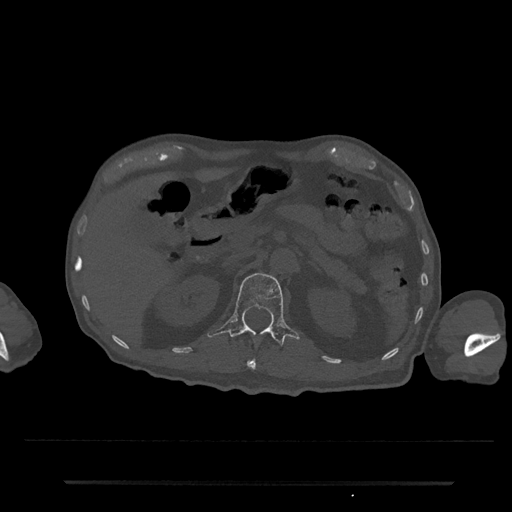
CT including the spine, one axial slice. Position 142 of 797 along the scan axis. Reconstruction kernel Br40s/3. Bone window (W 1800 / L 400 HU). 0.5 mm slice thickness. 512 × 512 image matrix, field of view 427 × 427 mm. Patient: male, 74 years. Case-level facts recorded for this patient, not image findings: primary cancer: prostate.
Structures marked on this image (semi-automatically segmented with operator editing):
- L1 vertebra: bounding box (x1, y1, x2, y2) in pixels: (207, 272, 300, 346)
- T12 vertebra: (247, 360, 256, 370)